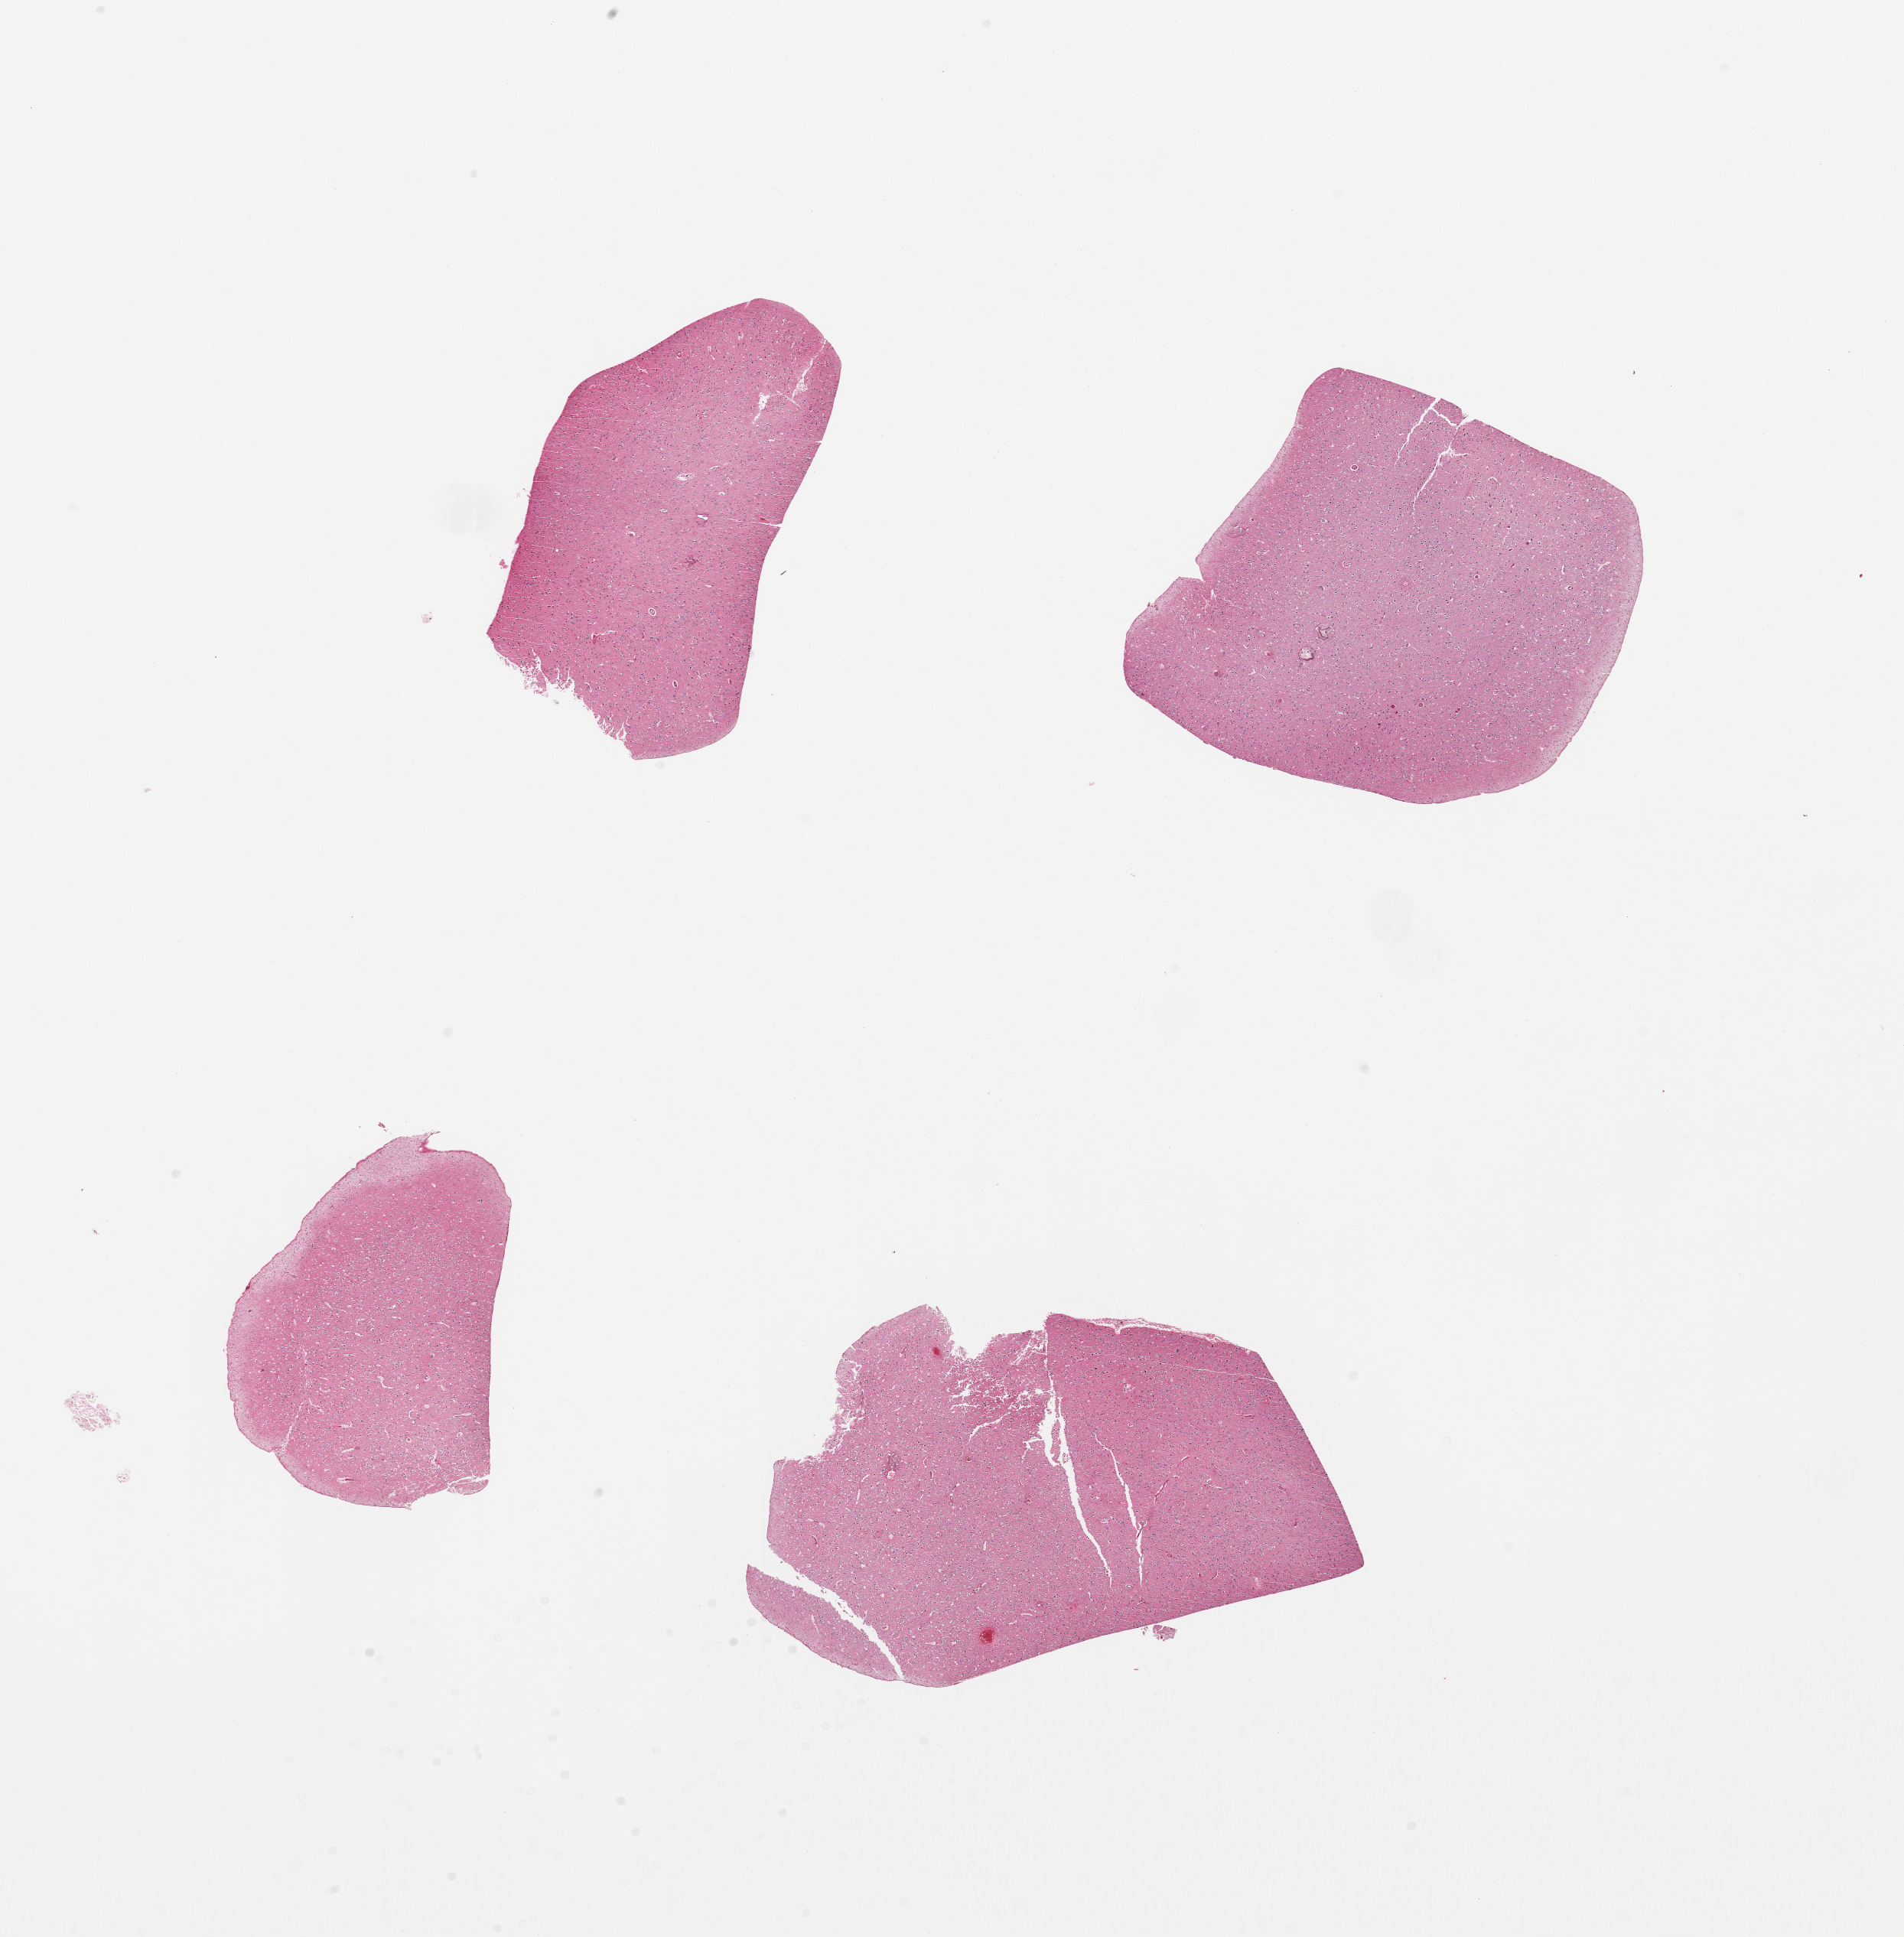
Whole-slide image, H&E stain, brightfield — low-resolution overview of the scanned area, about 19.7 x 20.0 mm, PAXgene-fixed, paraffin-embedded tissue, target tissue: cerebral cortex, donor tissue sample. Donor: male.
Reviewer comment on this tissue sample: 4 pieces.